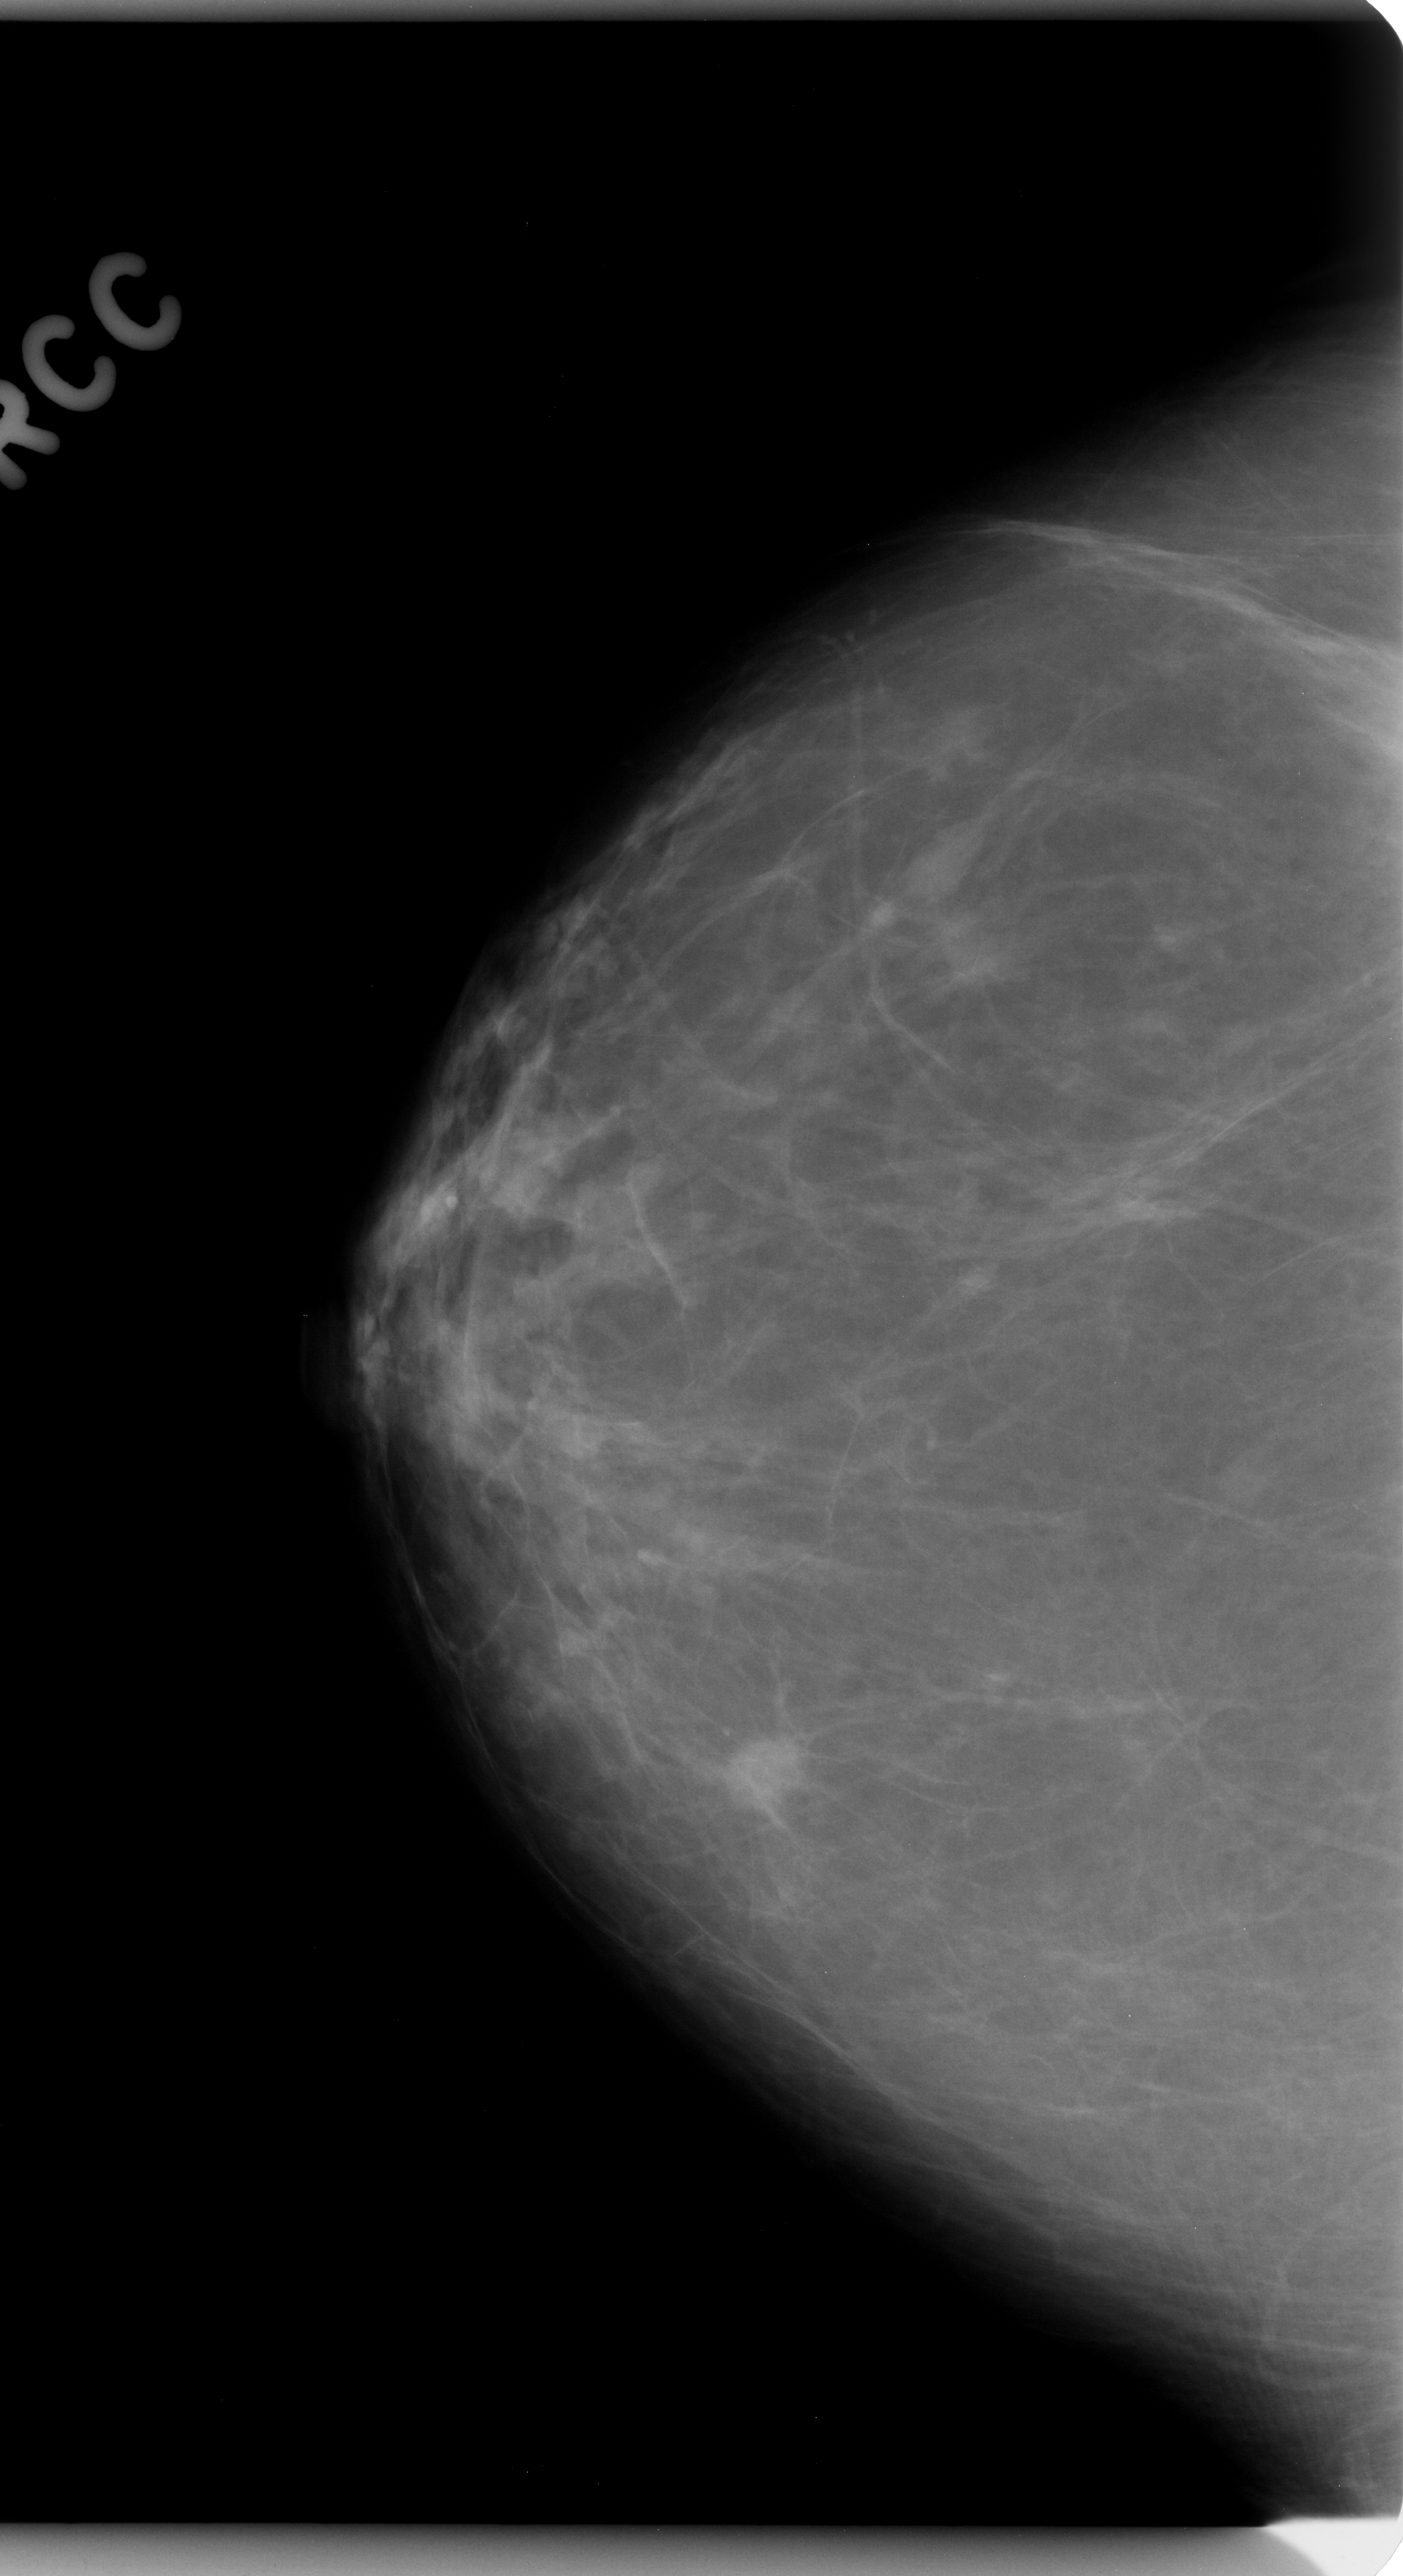
Scanned film-screen mammogram. Right breast. CC view. BI-RADS breast density category 1 (scale 1–4). 1403 × 2576 image matrix.
Expert-marked regions of interest on this film, with their recorded descriptors:
- mass, shape oval, margins spiculated; BI-RADS assessment category 5; pathology result (as recorded, not read from the image): malignant: box from (x=691, y=1699) to (x=843, y=1847) px